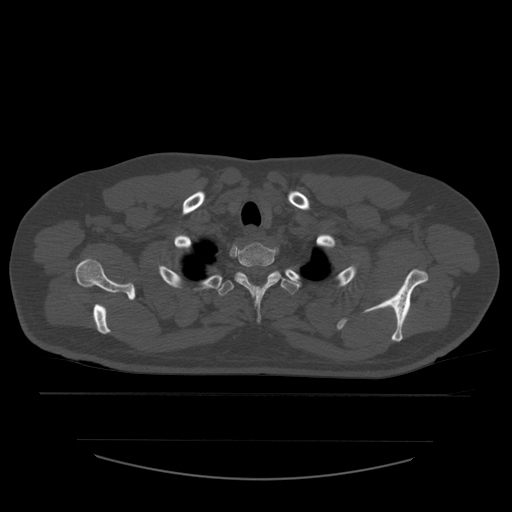
CT including the spine, one axial slice; slice 461 of 532 in the series (ordered by position); 120 kVp; bone window (W 1800 / L 400 HU); 512 × 512 image matrix, field of view 441 × 441 mm. Patient age 44 years. Case-level facts recorded for this patient, not image findings: primary cancer: soft tissue sarcoma.
Structures marked on this image (semi-automatic segmentation, software-assisted and operator-edited):
- T1 vertebra: box from (x=235, y=243) to (x=282, y=322) px
- T2 vertebra: (x=217, y=271)–(x=301, y=296)